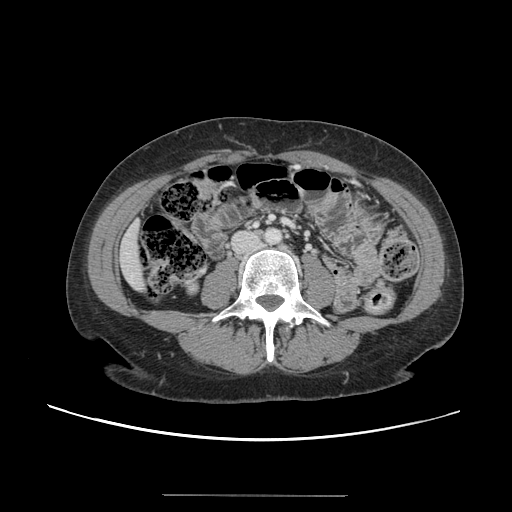
Contrast-enhanced abdominal CT, one axial slice; position 19 of 144 along the scan axis; intravenous contrast given; soft-tissue window (W 400 / L 40 HU); 2.5 mm slice thickness; 512 × 512 image matrix, field of view 380 × 380 mm. Female patient, age 53 years. Case-level facts recorded for this patient, not image findings: diagnosis: colorectal cancer liver metastases, imaged before liver resection; multiple liver metastases: yes; largest metastasis: 1.1 cm.
Annotated regions visible in this slice (expert manual segmentation):
- liver: bounding box [x1, y1, x2, y2] px = [119, 222, 144, 291]
- planned liver remnant (the part of the liver to remain after resection): [120, 223, 145, 292]